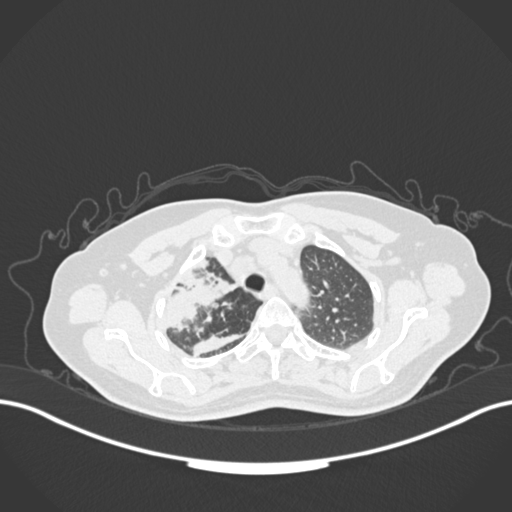
Chest CT, one axial slice; position 130 of 177 along the scan axis; reconstruction kernel B30f; lung window (W 1500 / L -600 HU); 1 mm slice thickness; 512 × 512 image matrix. Patient: female, 60 years. Case-level facts recorded for this patient, not image findings: clinical TNM (as recorded): T3 N1 M1.
Annotated regions visible in this slice (rectangle marked by the reading radiologist):
- lung tumour (recorded histology: adenocarcinoma): bounding box (x1, y1, x2, y2) in pixels: (153, 257, 237, 336)